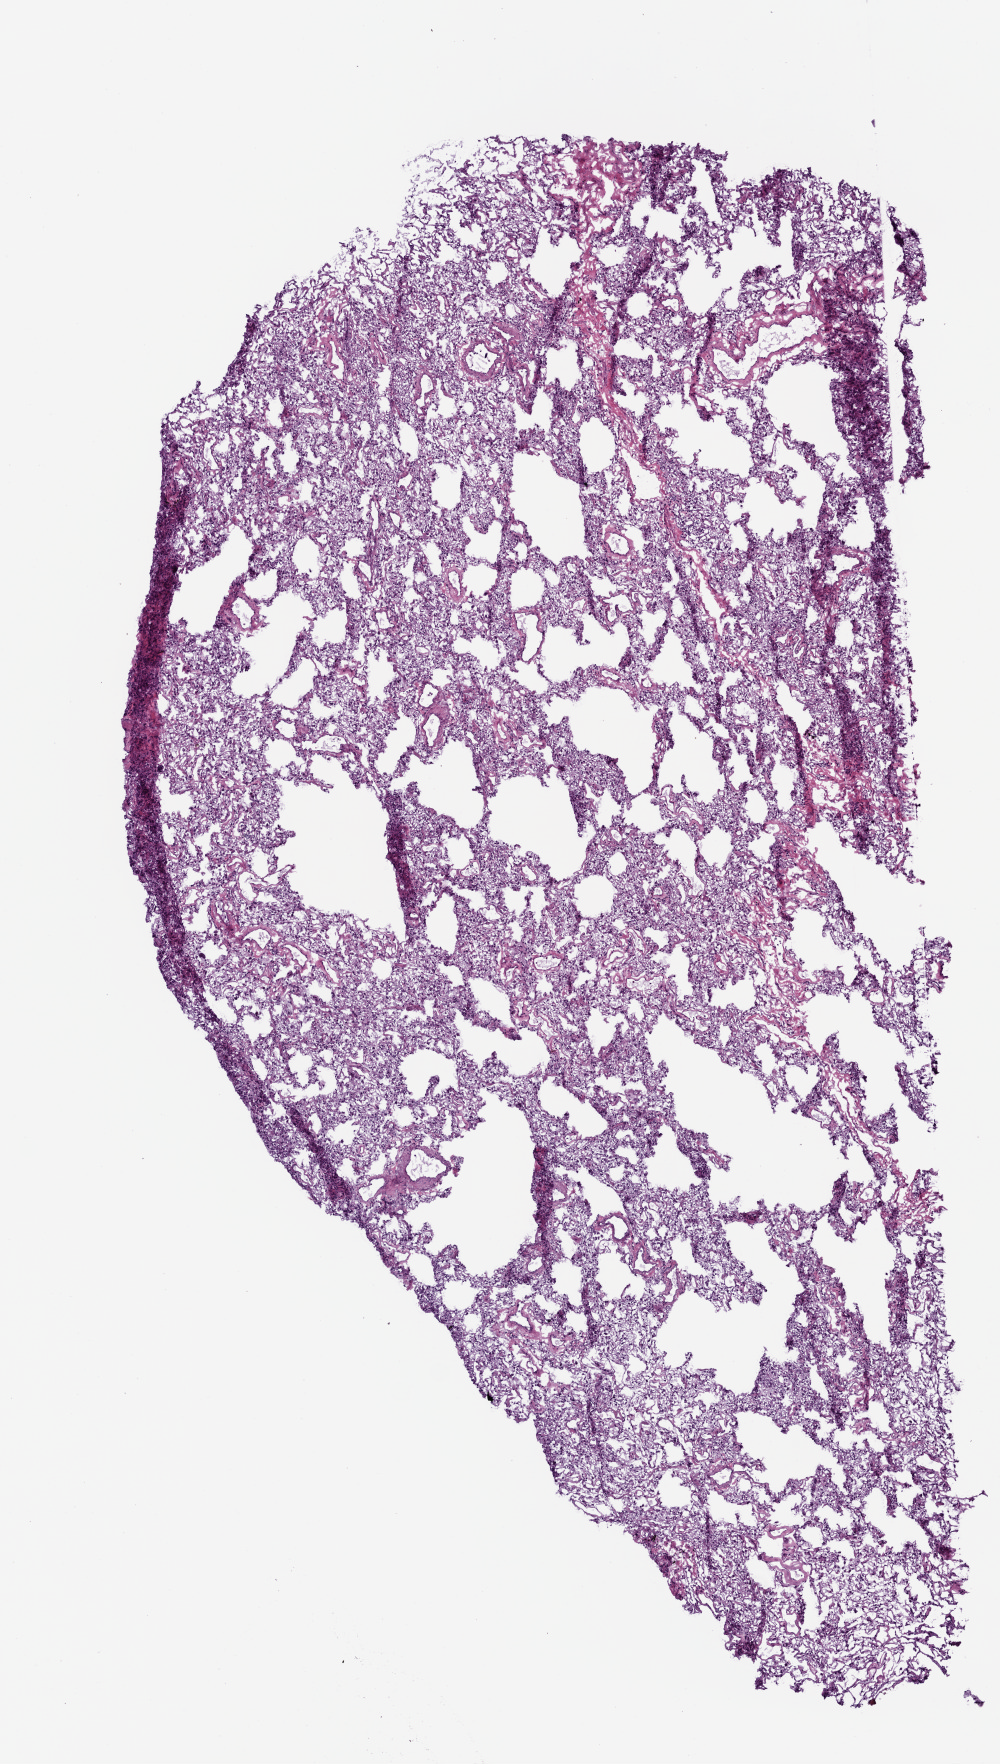
H&E whole-slide image — whole scanned area (about 4.0 x 7.1 mm, acquisition: 20x scan) shown as a low-resolution overview. Frozen section from the top of the tissue portion. Solid tissue normal (non-tumour tissue) sample from the lung. Male patient; age at initial diagnosis 57 years.
This section: solid tissue normal (non-tumour) sample from the same patient. Patient diagnosis: Squamous cell carcinoma, NOS (upper lobe, lung).